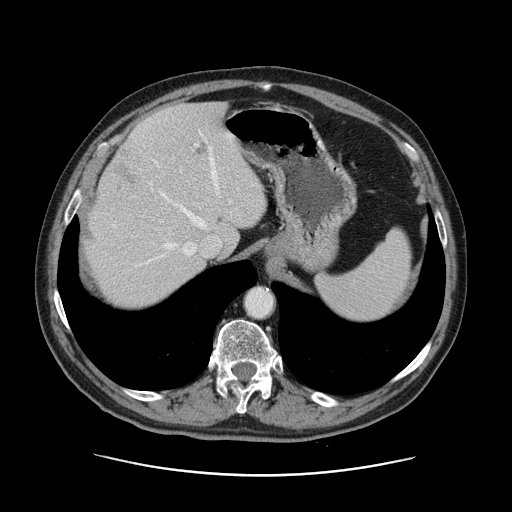
Contrast-enhanced abdominal CT, one axial slice. Position 100 of 141 along the scan axis. Intravenous contrast given. Soft-tissue window (W 400 / L 40 HU). 2.5 mm slice thickness. 512 × 512 image matrix, field of view 395 × 395 mm. Male patient, age 72 years. Case-level facts recorded for this patient, not image findings: diagnosis: colorectal cancer liver metastases, imaged before liver resection; multiple liver metastases: yes; largest metastasis: 5.4 cm; chemotherapy before resection: yes.
Outlined on this slice (outlined manually by an expert reader):
- hepatic veins: box from (x=138, y=135) to (x=218, y=266) px
- liver: (x=88, y=102)–(x=267, y=311)
- planned liver remnant (the part of the liver to remain after resection): (x=92, y=102)–(x=267, y=311)
- portal vein (with intrahepatic branches): (x=189, y=143)–(x=232, y=250)
- liver metastasis: (x=112, y=150)–(x=134, y=183)